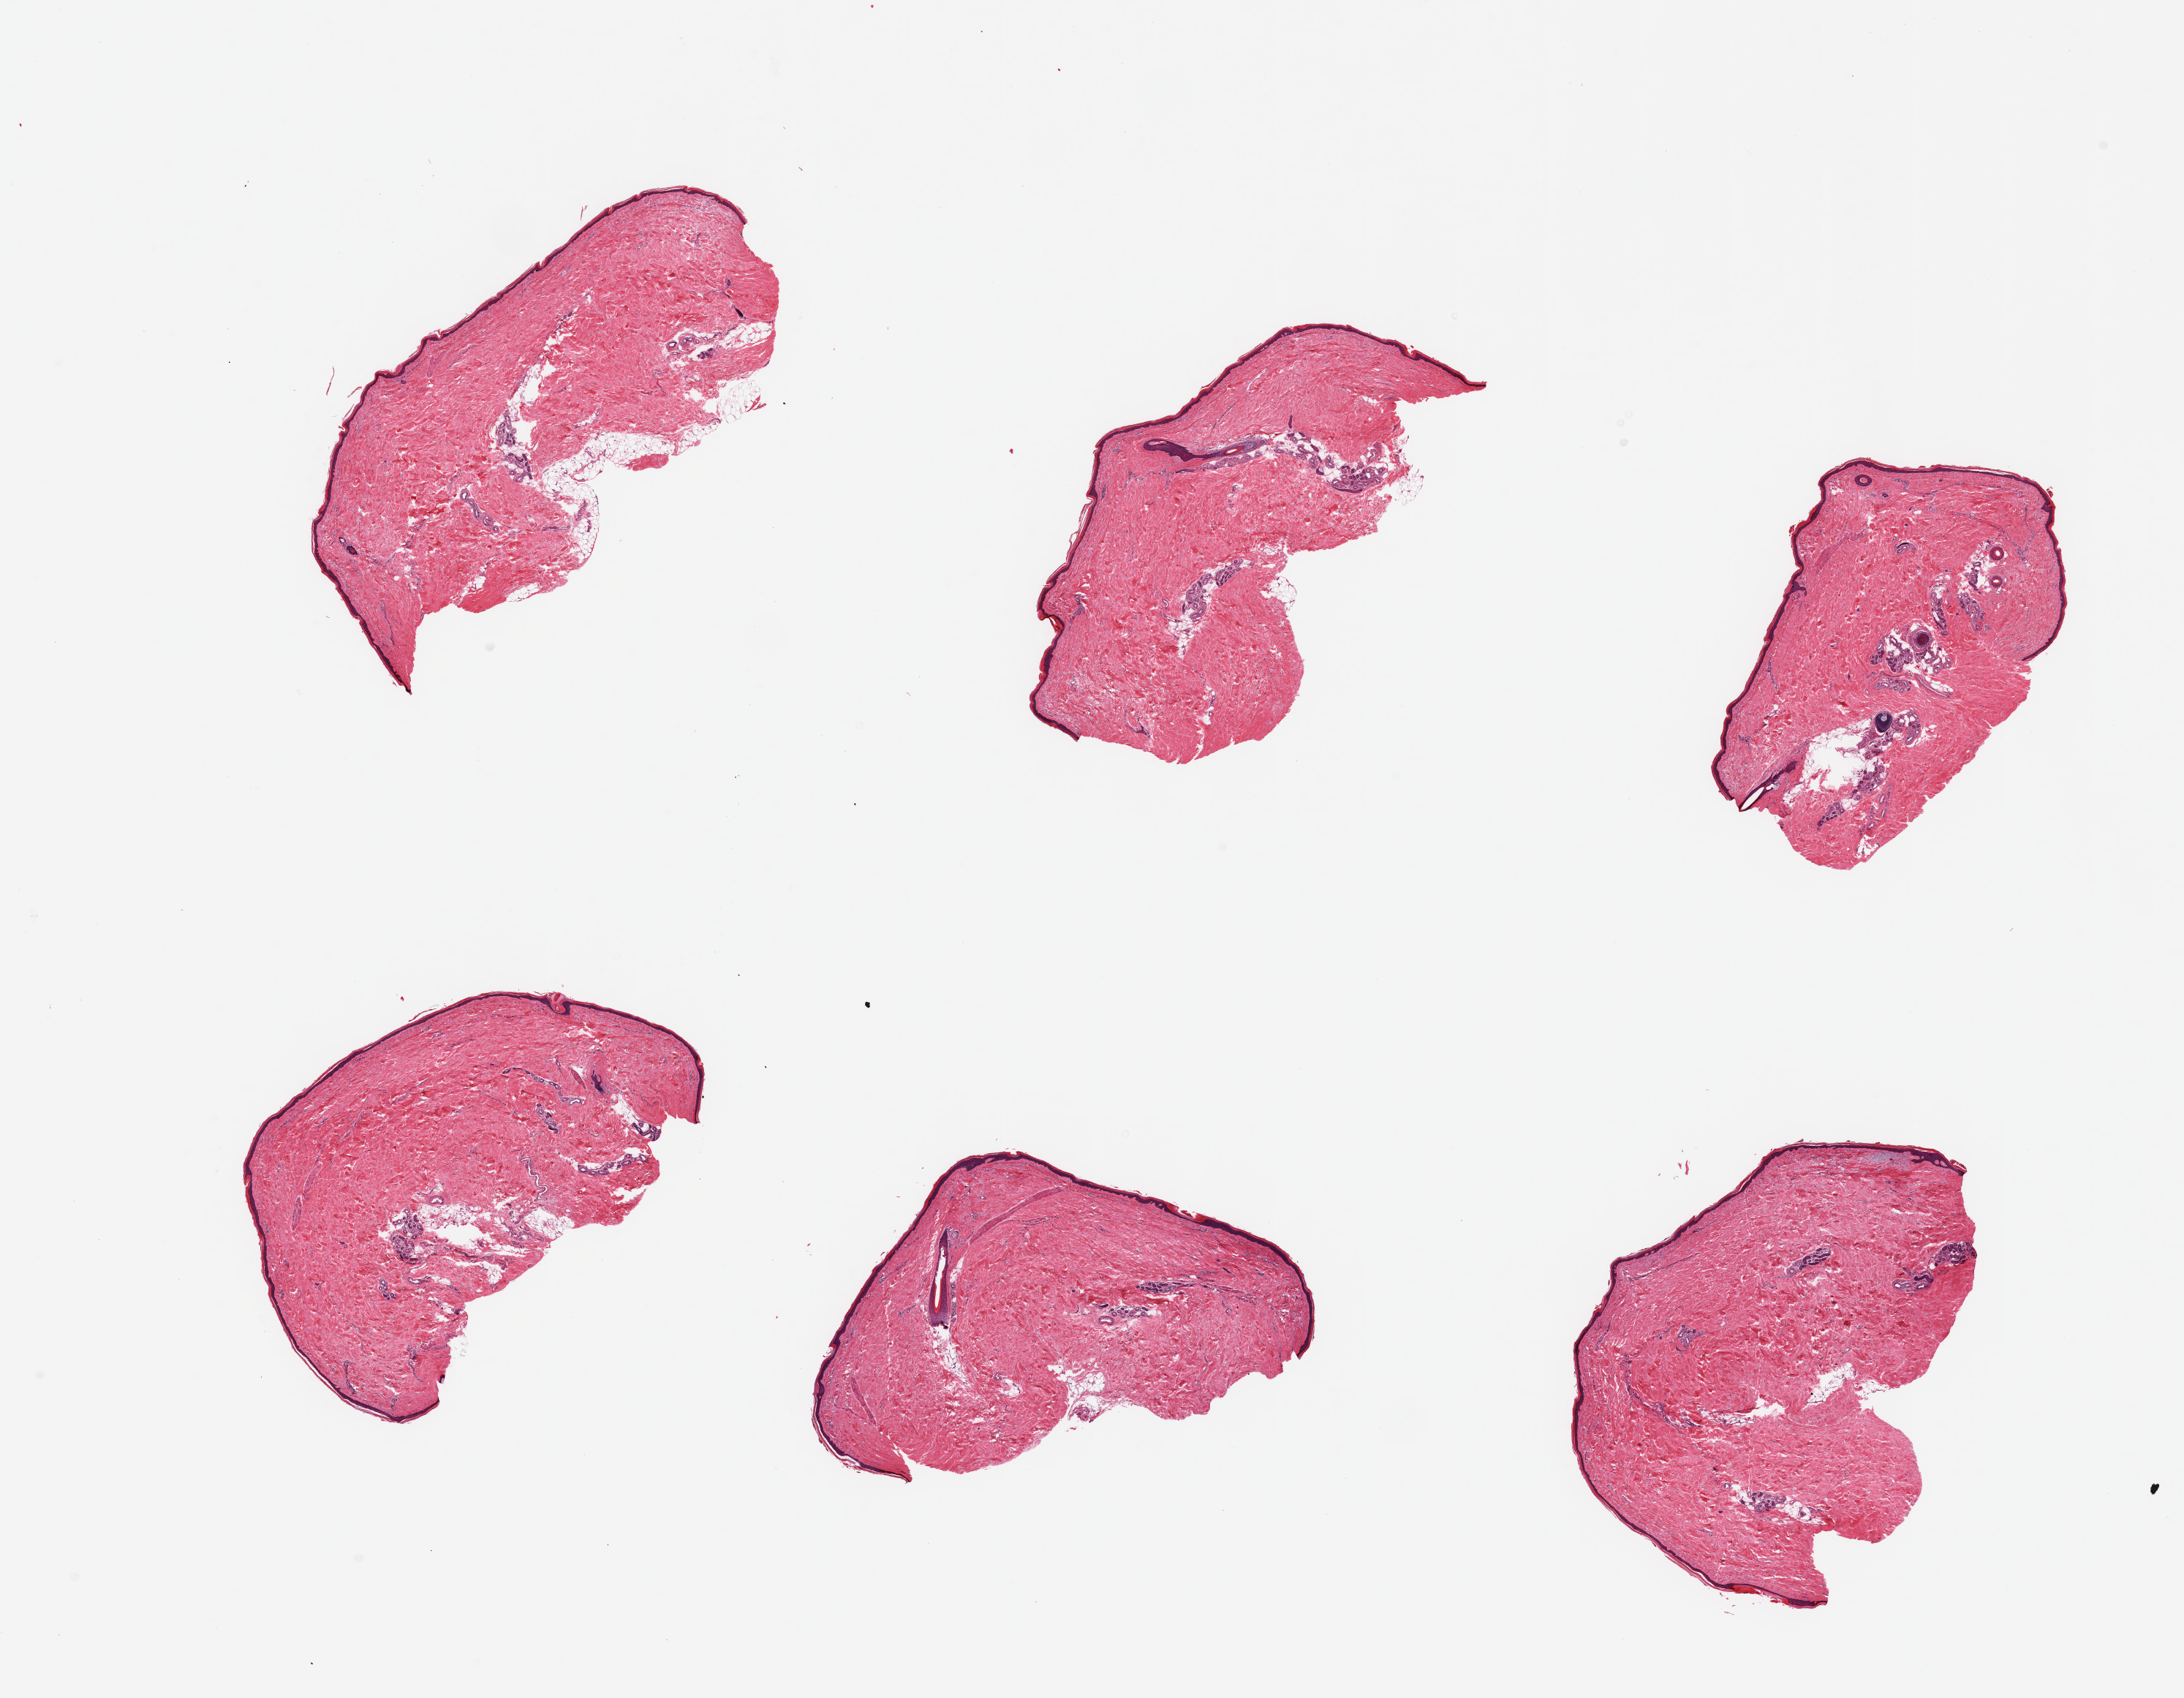
Hematoxylin and eosin (H&E) whole-slide image — whole scanned area (about 23.6 x 18.4 mm, slide scanned at 20x) shown as a low-resolution overview; PAXgene-fixed, paraffin-embedded tissue; sampled site (target tissue): skin of lower leg; donor tissue sample. Donor: male.
Review note (as recorded): 6 pieces, no dermal fat; squamous epithelium is ~ 35-40 microns.